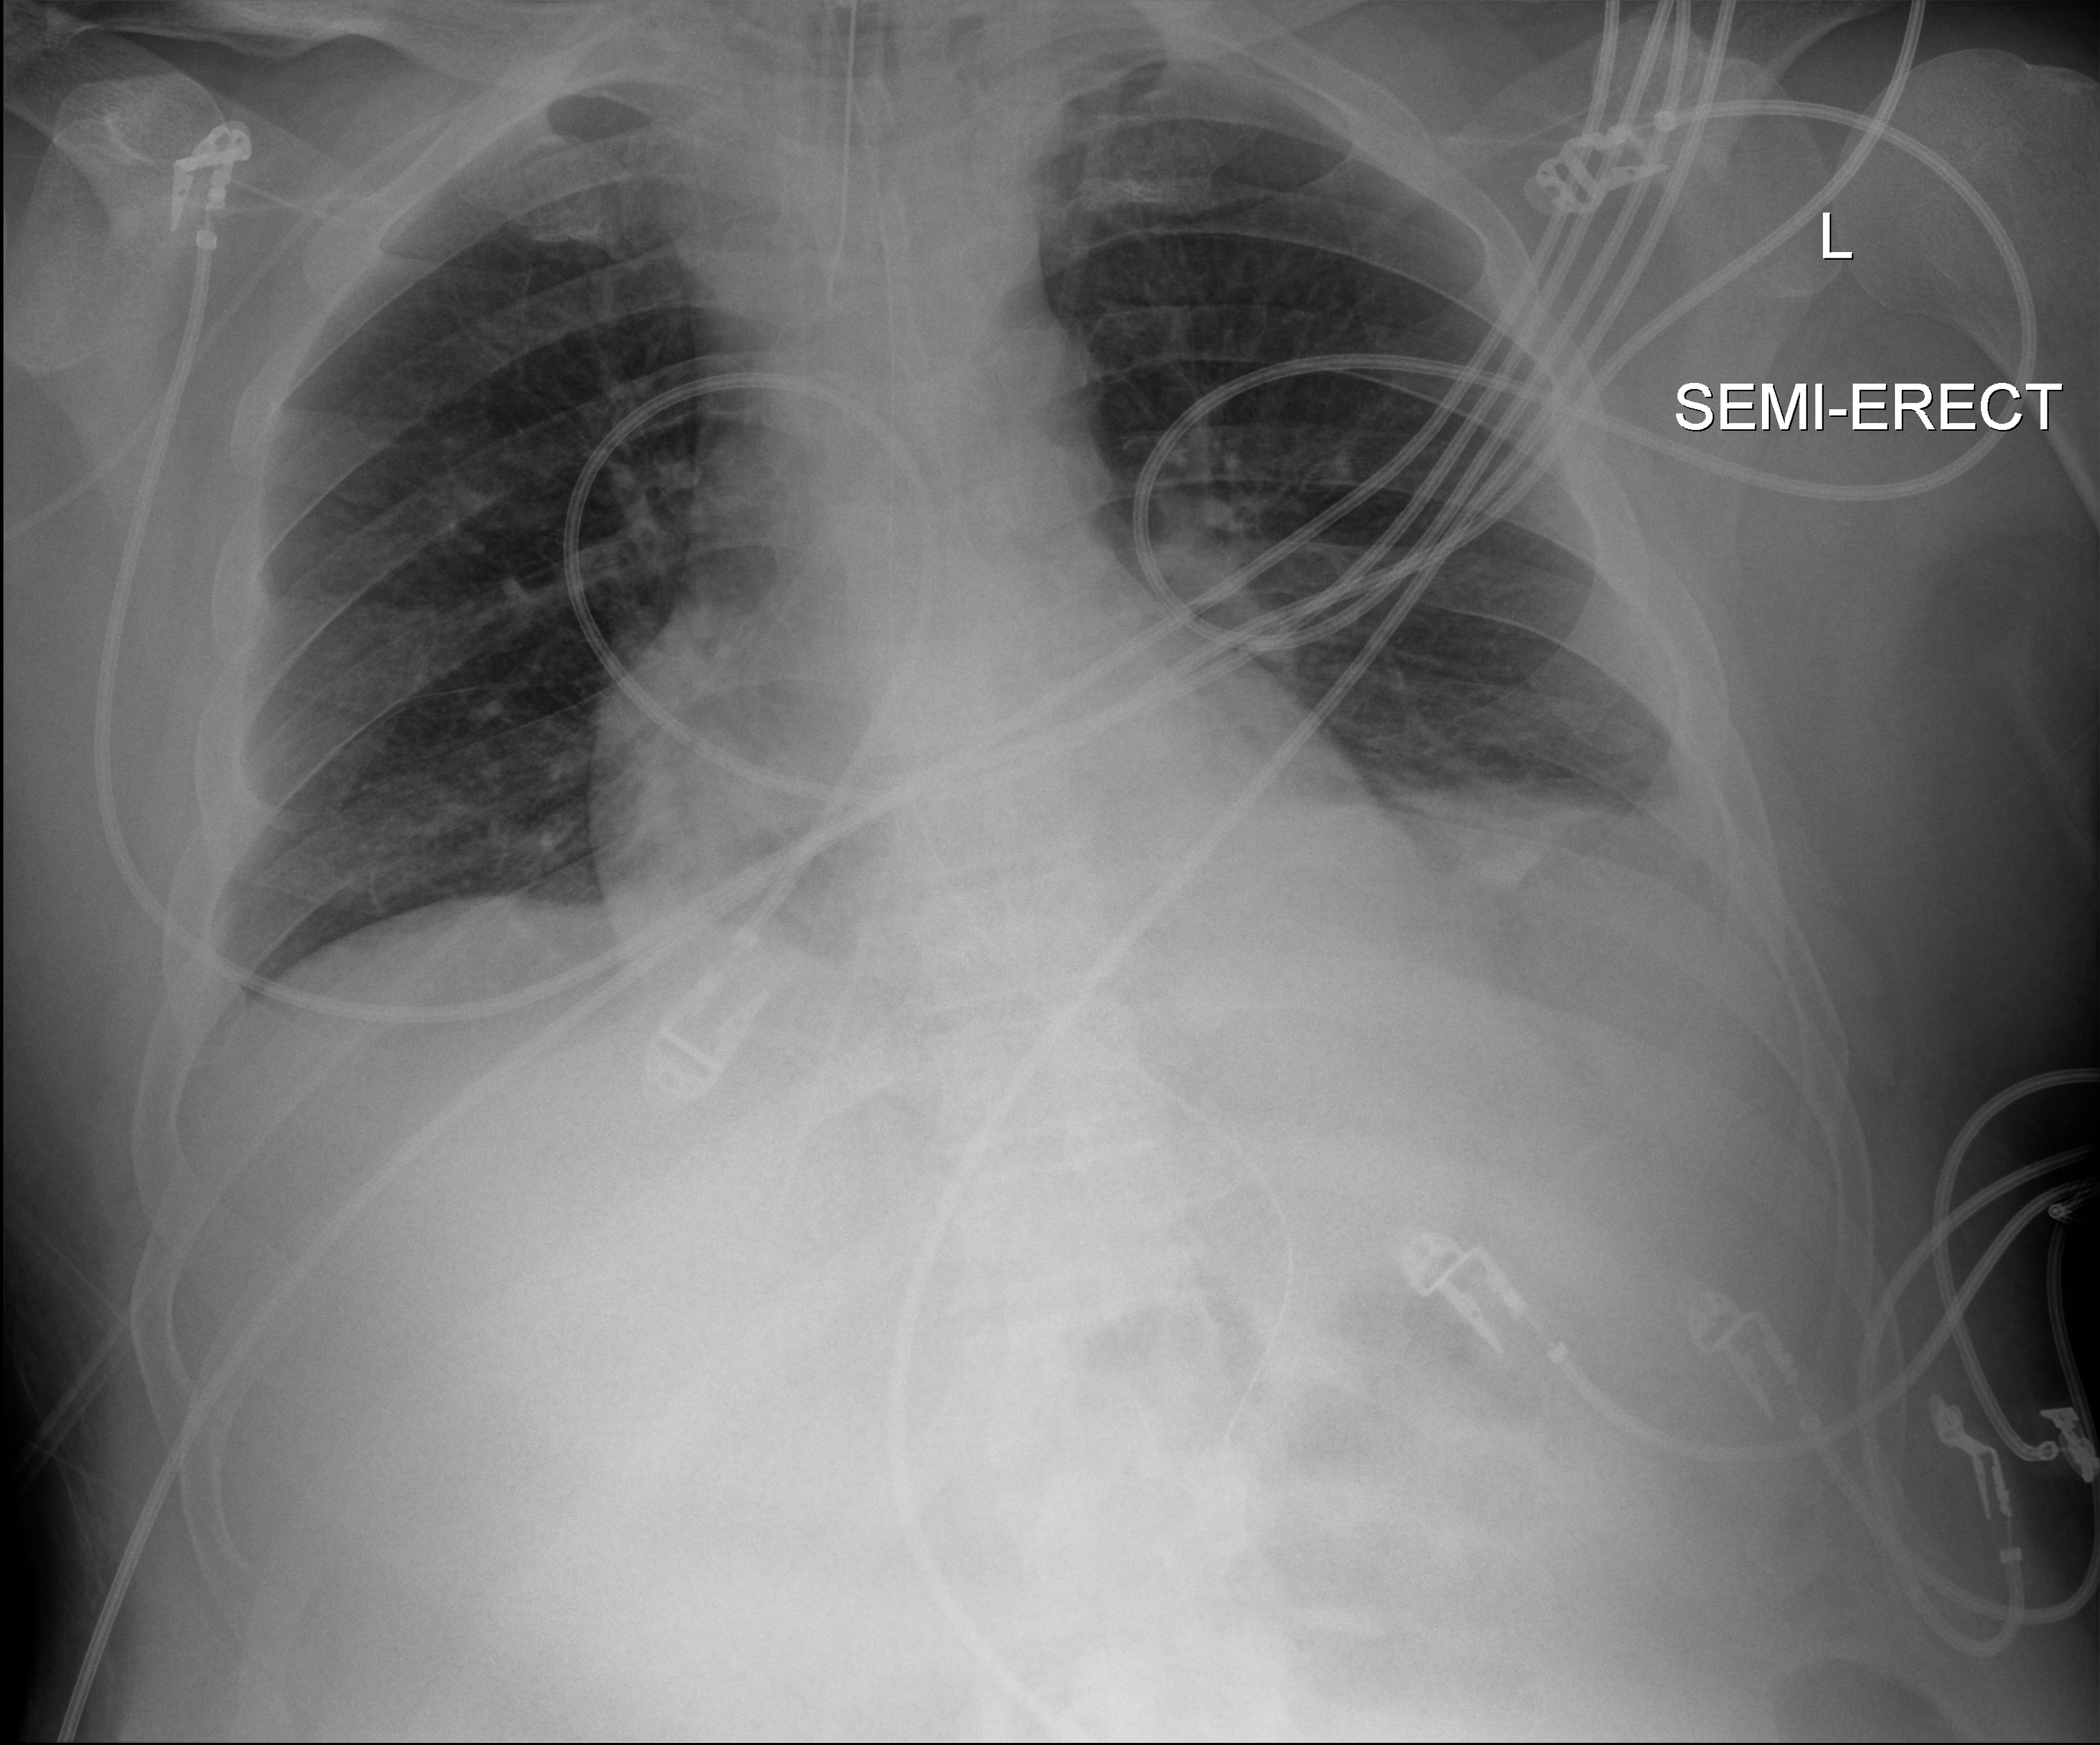
Bedside chest radiograph (digital radiography); anteroposterior (AP) projection. Patient hospitalised with COVID-19; male, aged 18–59 years.
From the hospital-stay record, not from the radiograph (when in the stay this image was taken is not recorded):
- length of hospital stay: 65 days